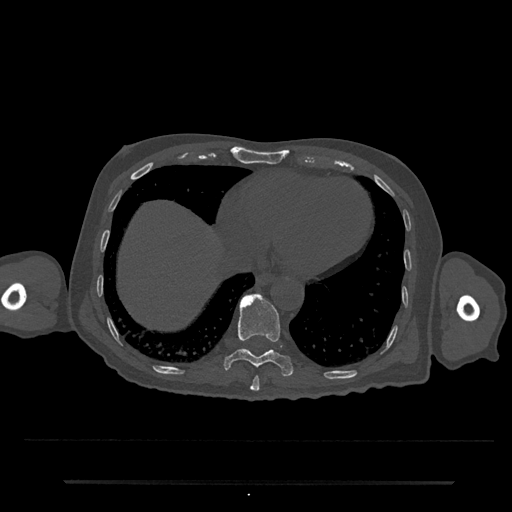
CT including the spine, one axial slice. Position 314 of 797 along the scan axis. 120 kVp. Bone window (W 1800 / L 400 HU). 0.5 mm slice thickness. 512 × 512 image matrix. Male patient, age 74 years. From the clinical record (not read from this slice): primary cancer: prostate.
Outlined on this slice (semi-automatically segmented with operator editing):
- T10 vertebra: bounding box [x1, y1, x2, y2] px = [224, 293, 294, 377]
- T9 vertebra: [250, 376, 260, 392]